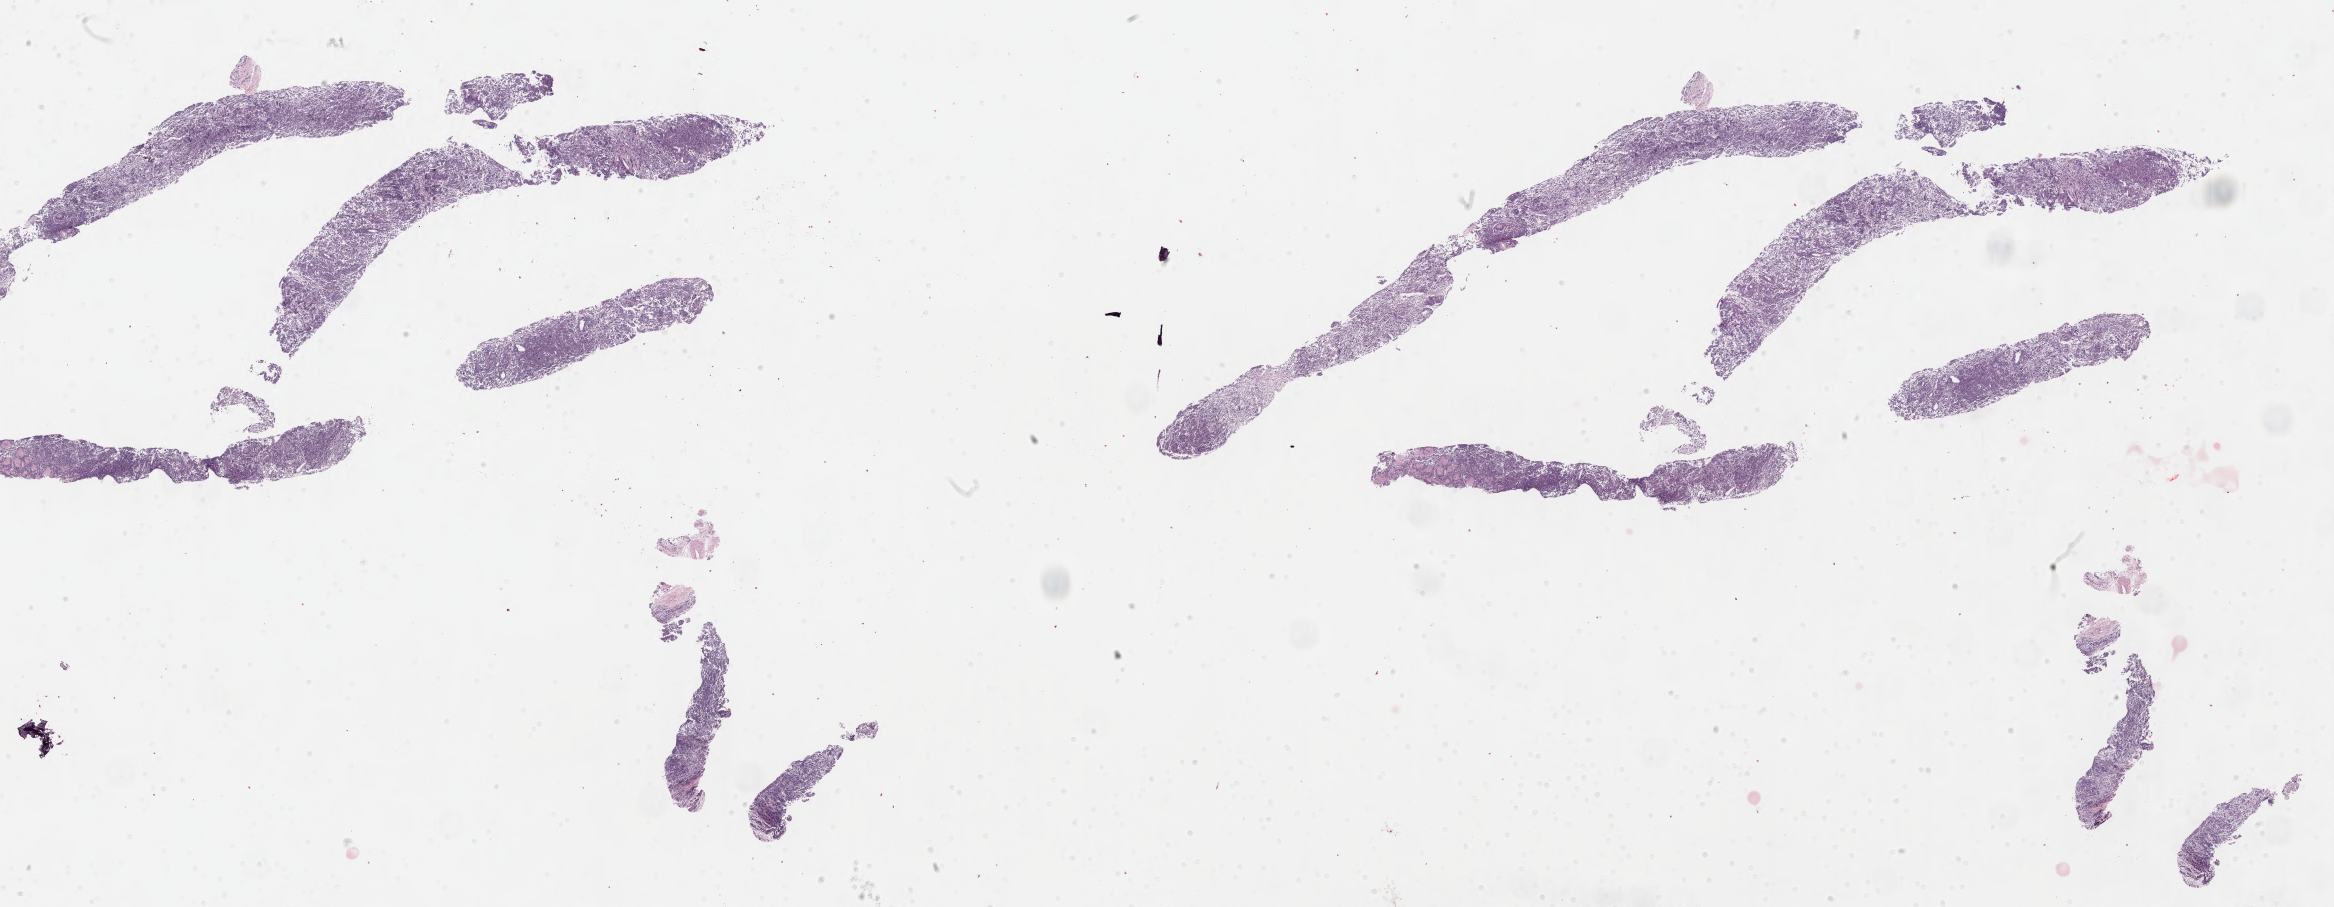
Digitized haematoxylin and eosin-stained section, low-resolution overview of the scanned area, about 37.7 x 14.7 mm. Specimen: tumor tissue. Patient male; aged 66.
Histologic diagnosis: Burkitt lymphoma, NOS.